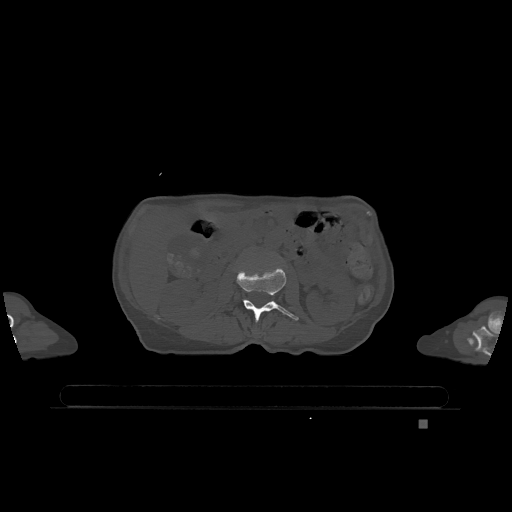
CT including the spine, one axial slice; position 410 of 1317 along the scan axis; bone window (W 1800 / L 400 HU); 512 × 512 image matrix. Patient: female, 74 years. Case-level facts recorded for this patient, not image findings: primary cancer: lung.
Outlined on this slice (semi-automatic segmentation, software-assisted and operator-edited):
- L2 vertebra: bounding box [x1, y1, x2, y2] px = [237, 266, 299, 322]